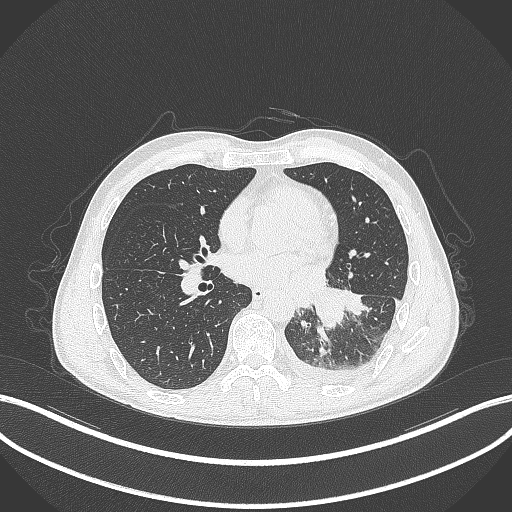
Chest CT, one axial slice; position 139 of 295 along the scan axis; reconstruction kernel B70f; 120 kVp; lung window (W 1500 / L -600 HU); 1 mm slice thickness; 512 × 512 image matrix. Male patient, age 47 years. Case-level facts recorded for this patient, not image findings: clinical TNM (as recorded): T3 N1 M1c; histopathological grade: G3.
Structures marked on this image (bounding box drawn by a radiologist):
- lung tumour (recorded histology: small cell carcinoma): bounding box <310,285,344,331> (left, top, right, bottom; pixels)